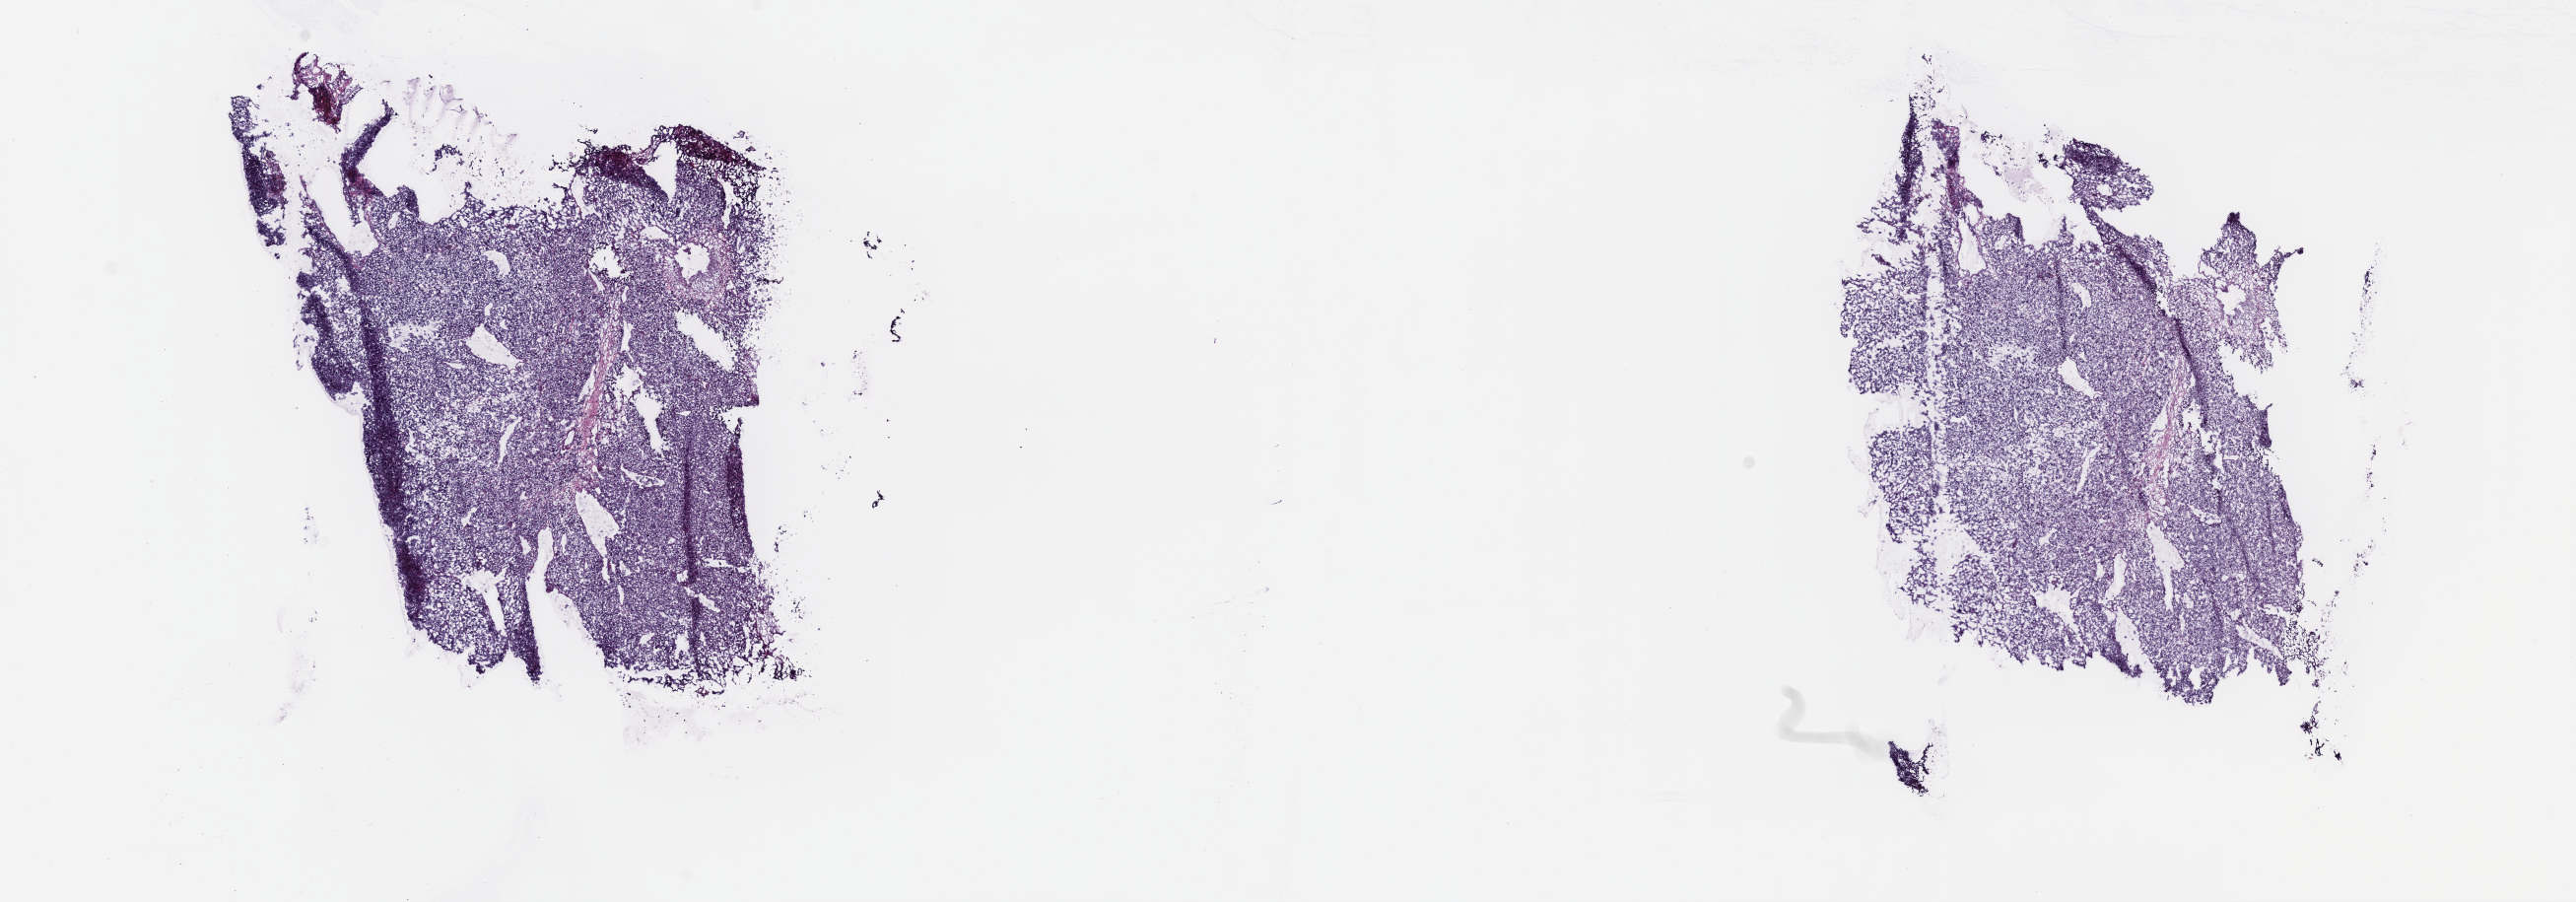
Whole-slide histology image, H&E — whole scanned area (about 21.1 x 7.4 mm, acquisition: 40x scan) shown as a low-resolution overview. Frozen section from the top of the tissue portion. Primary tumour sample from the adrenal gland. Female, age 25 years at initial diagnosis. Pathologist review of this section (percent, as recorded): tumour cells 80%, tumour nuclei 80%.
Pathologic diagnosis: Pheochromocytoma, malignant.